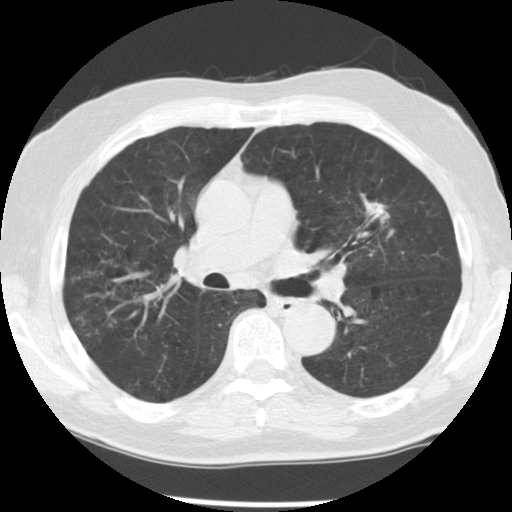
Low-dose screening chest CT, one axial slice; position 75 of 131 along the scan axis; reconstruction kernel STANDARD; lung window (W 1500 / L -600 HU); 2.5 mm slice thickness; 512 × 512 image matrix, field of view 330 × 330 mm.
Annotated regions visible in this slice (manually delineated by an expert):
- lesion 1 (tumor, upper lobe of left lung): bounding box [x1, y1, x2, y2] px = [372, 203, 390, 223]